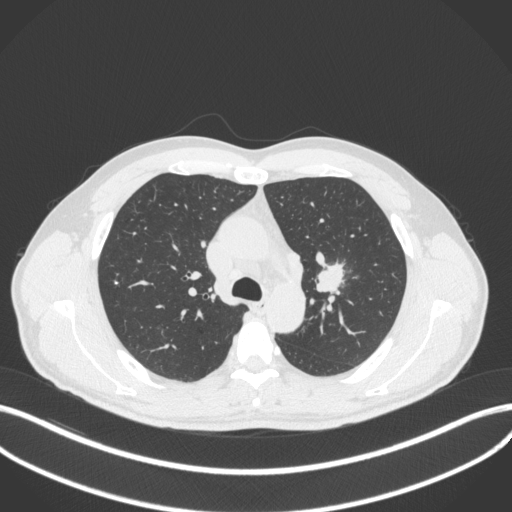
Chest CT, one axial slice; slice 292 of 383 in the series (ordered by position); reconstruction kernel B31f; 120 kVp; lung window (W 1500 / L -600 HU); 1 mm slice thickness; 512 × 512 image matrix. Male patient, age 50 years. Case-level facts recorded for this patient, not image findings: clinical TNM (as recorded): T1c N1 M1b.
Outlined on this slice (bounding box drawn by a radiologist):
- lung tumour (recorded histology: squamous cell carcinoma): bounding box <314,259,346,295> (left, top, right, bottom; pixels)